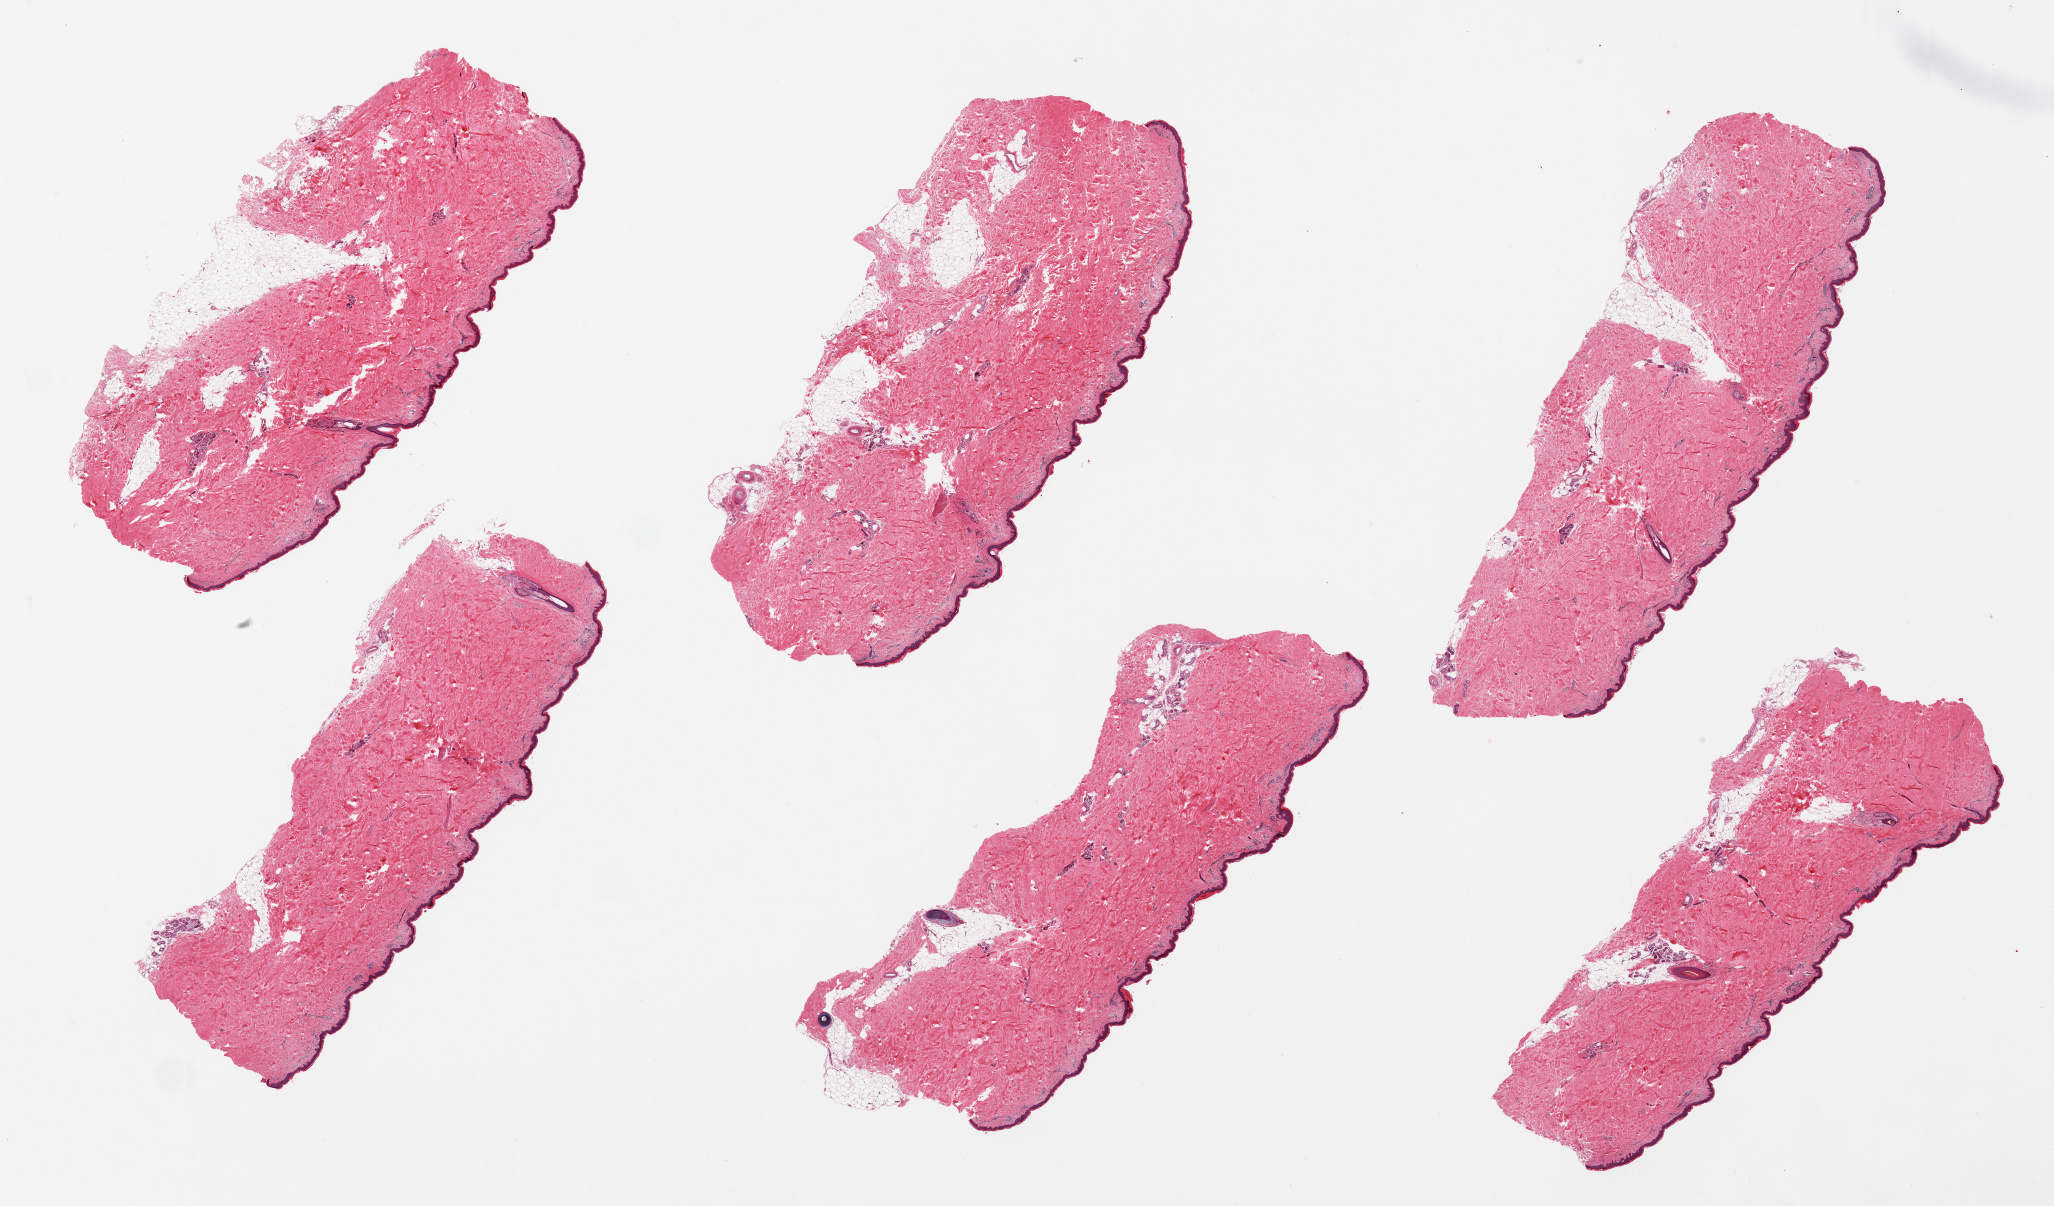
H&E whole-slide image — whole scanned area (about 32.5 x 19.1 mm, from a 20x scan) shown as a low-resolution overview; PAXgene-fixed paraffin-embedded (PFPE) section; section of skin of lower leg (target tissue); donor tissue sample. Donor: male.
Pathologist's review note for this sample: 6 pieces; well-trimmed, squamous epithelium measures ~ 1-1.5% of thickness.